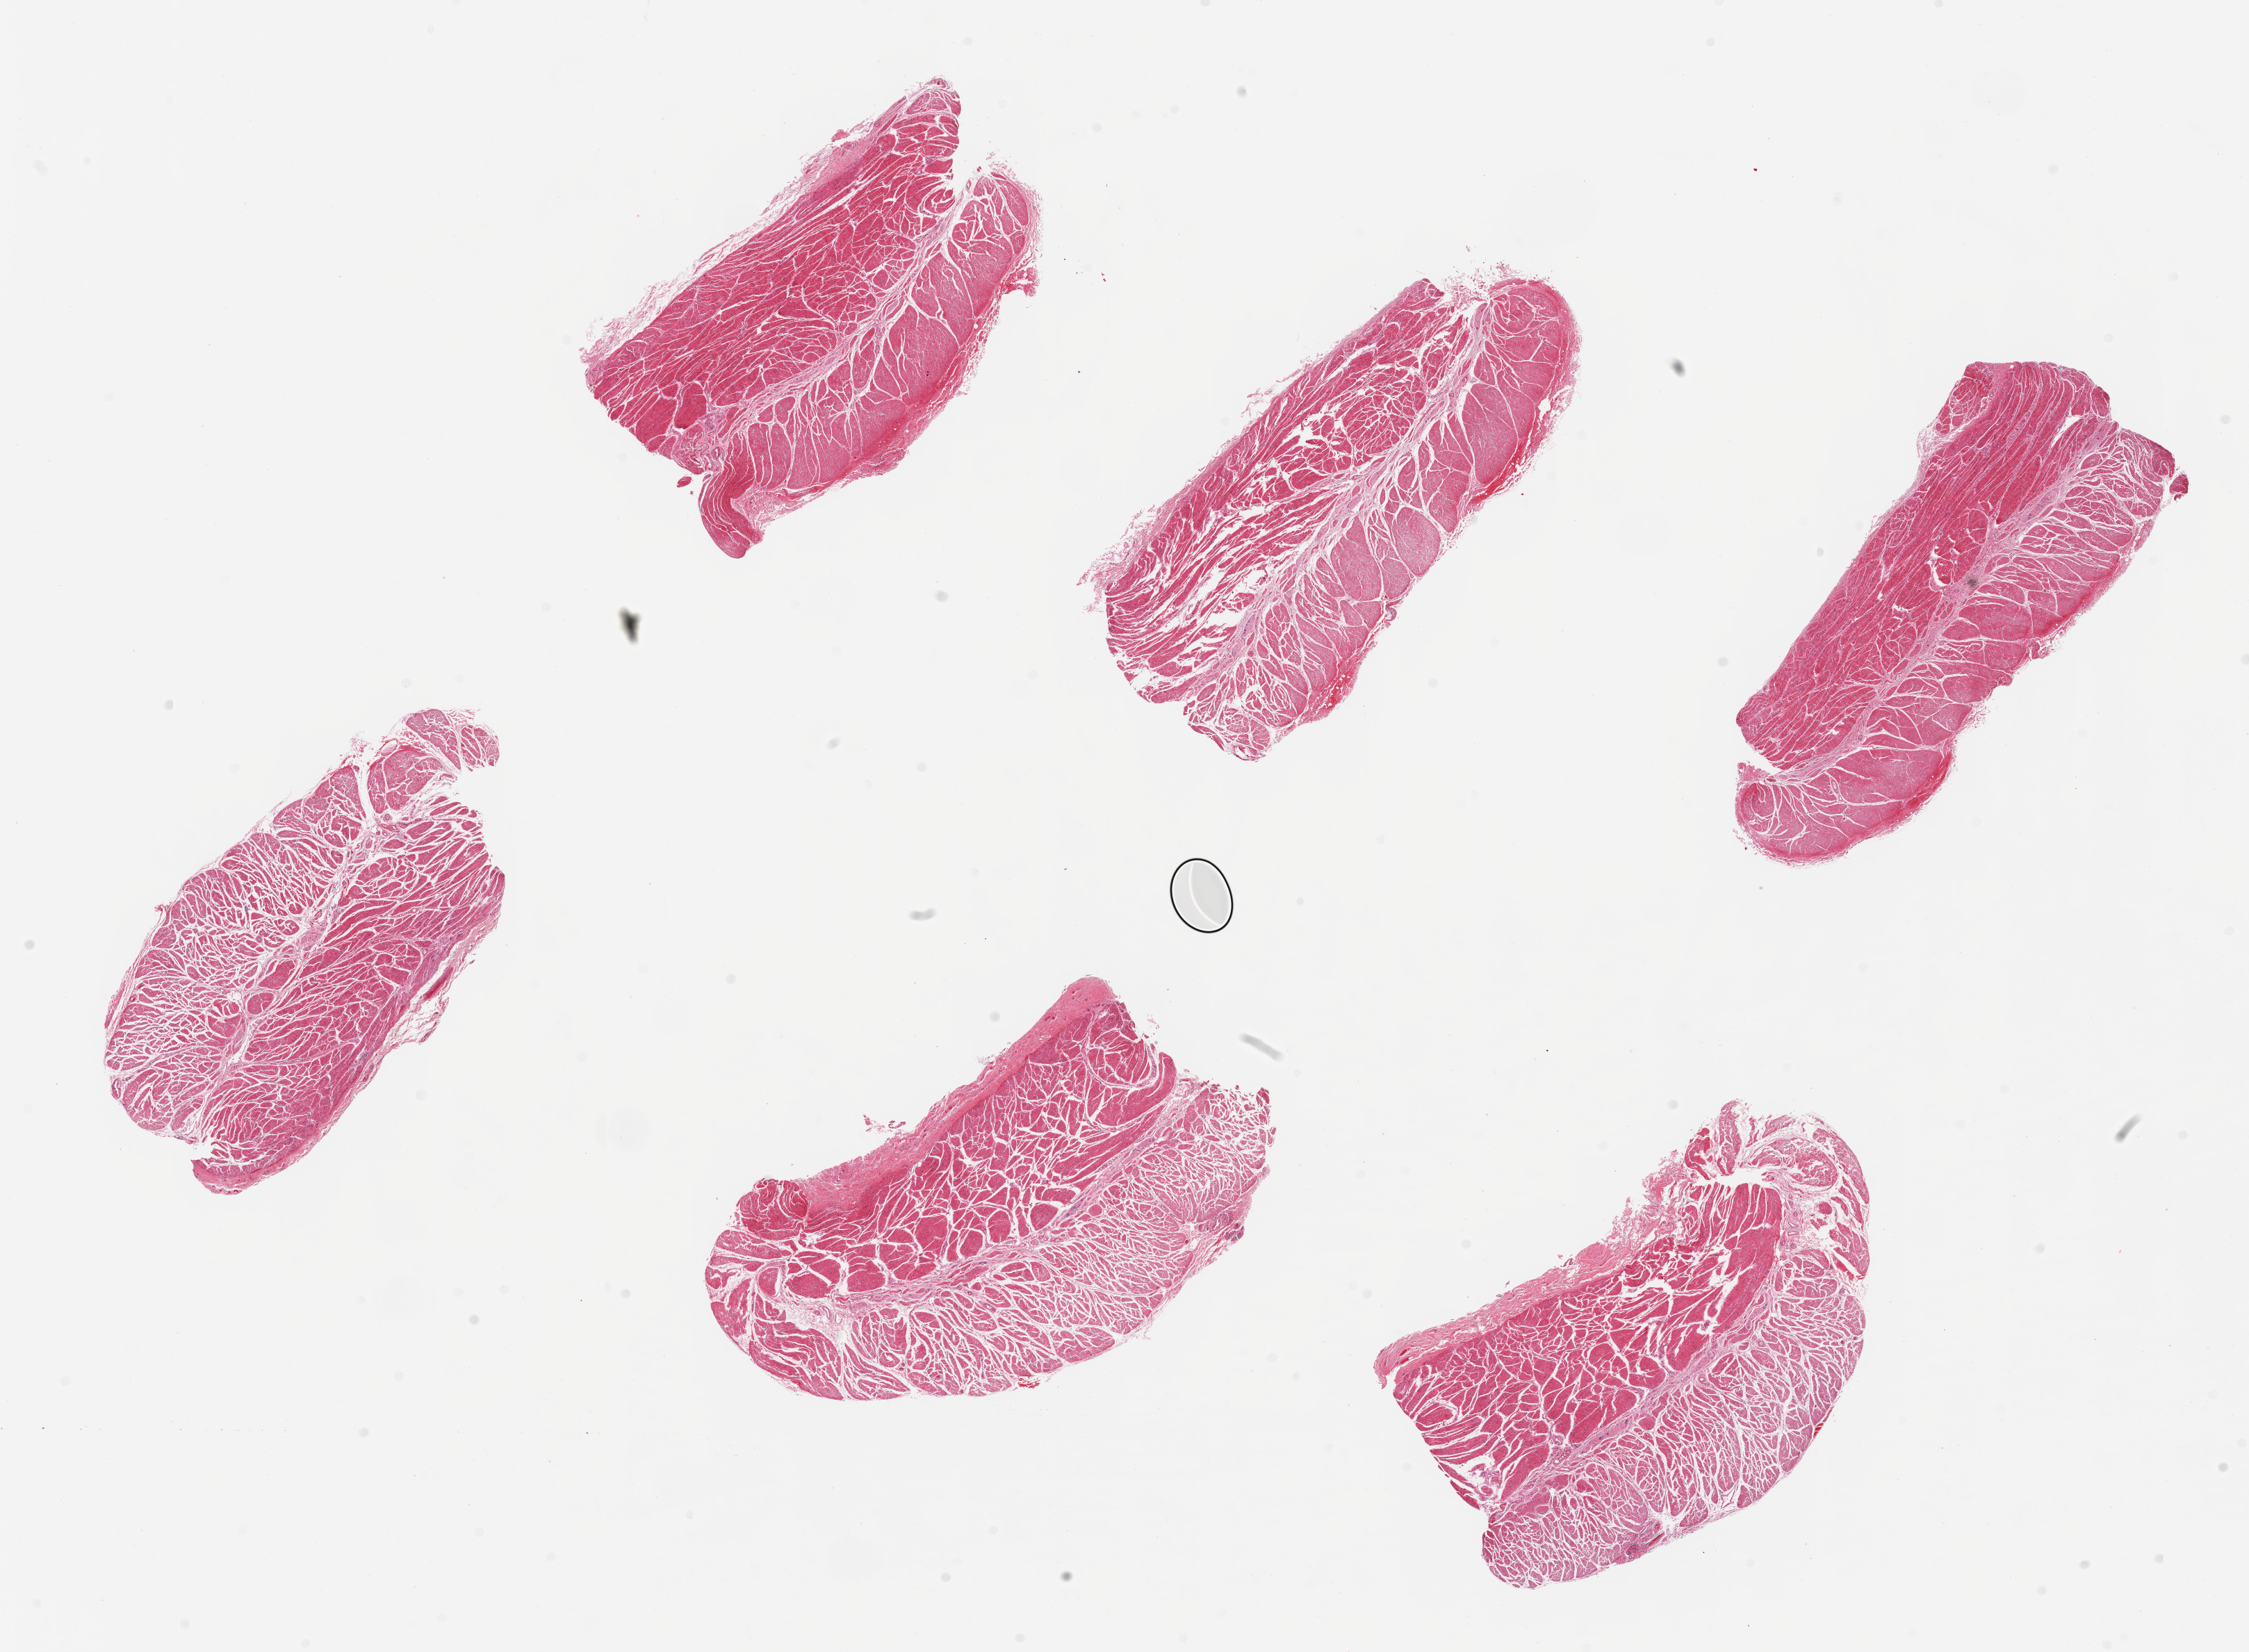
Haematoxylin and eosin whole-slide image, low-resolution overview of the scanned area, about 25.6 x 18.8 mm; PAXgene-fixed paraffin-embedded (PFPE) section; section of esophageal muscle (target tissue); donor tissue sample. Donor: male.
- review note (as recorded): 6 pieces, all muscularis